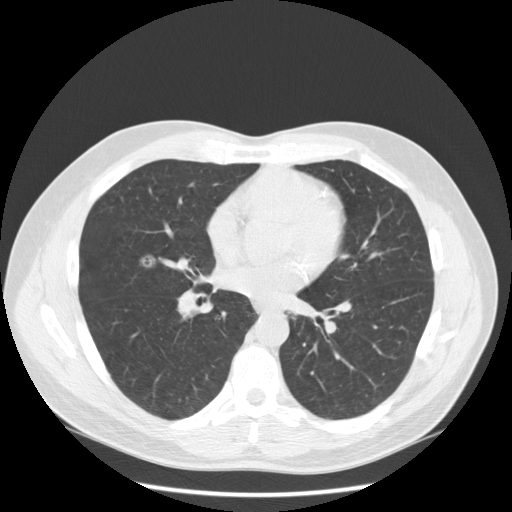
Low-dose screening chest CT, one axial slice; slice 107 of 234 in the series (ordered by position); lung window (W 1500 / L -600 HU); 512 × 512 image matrix.
Outlined on this slice (expert manual segmentation):
- lesion 1 (tumor, middle lobe of right lung): bounding box (x1, y1, x2, y2) in pixels: (140, 254, 156, 268)